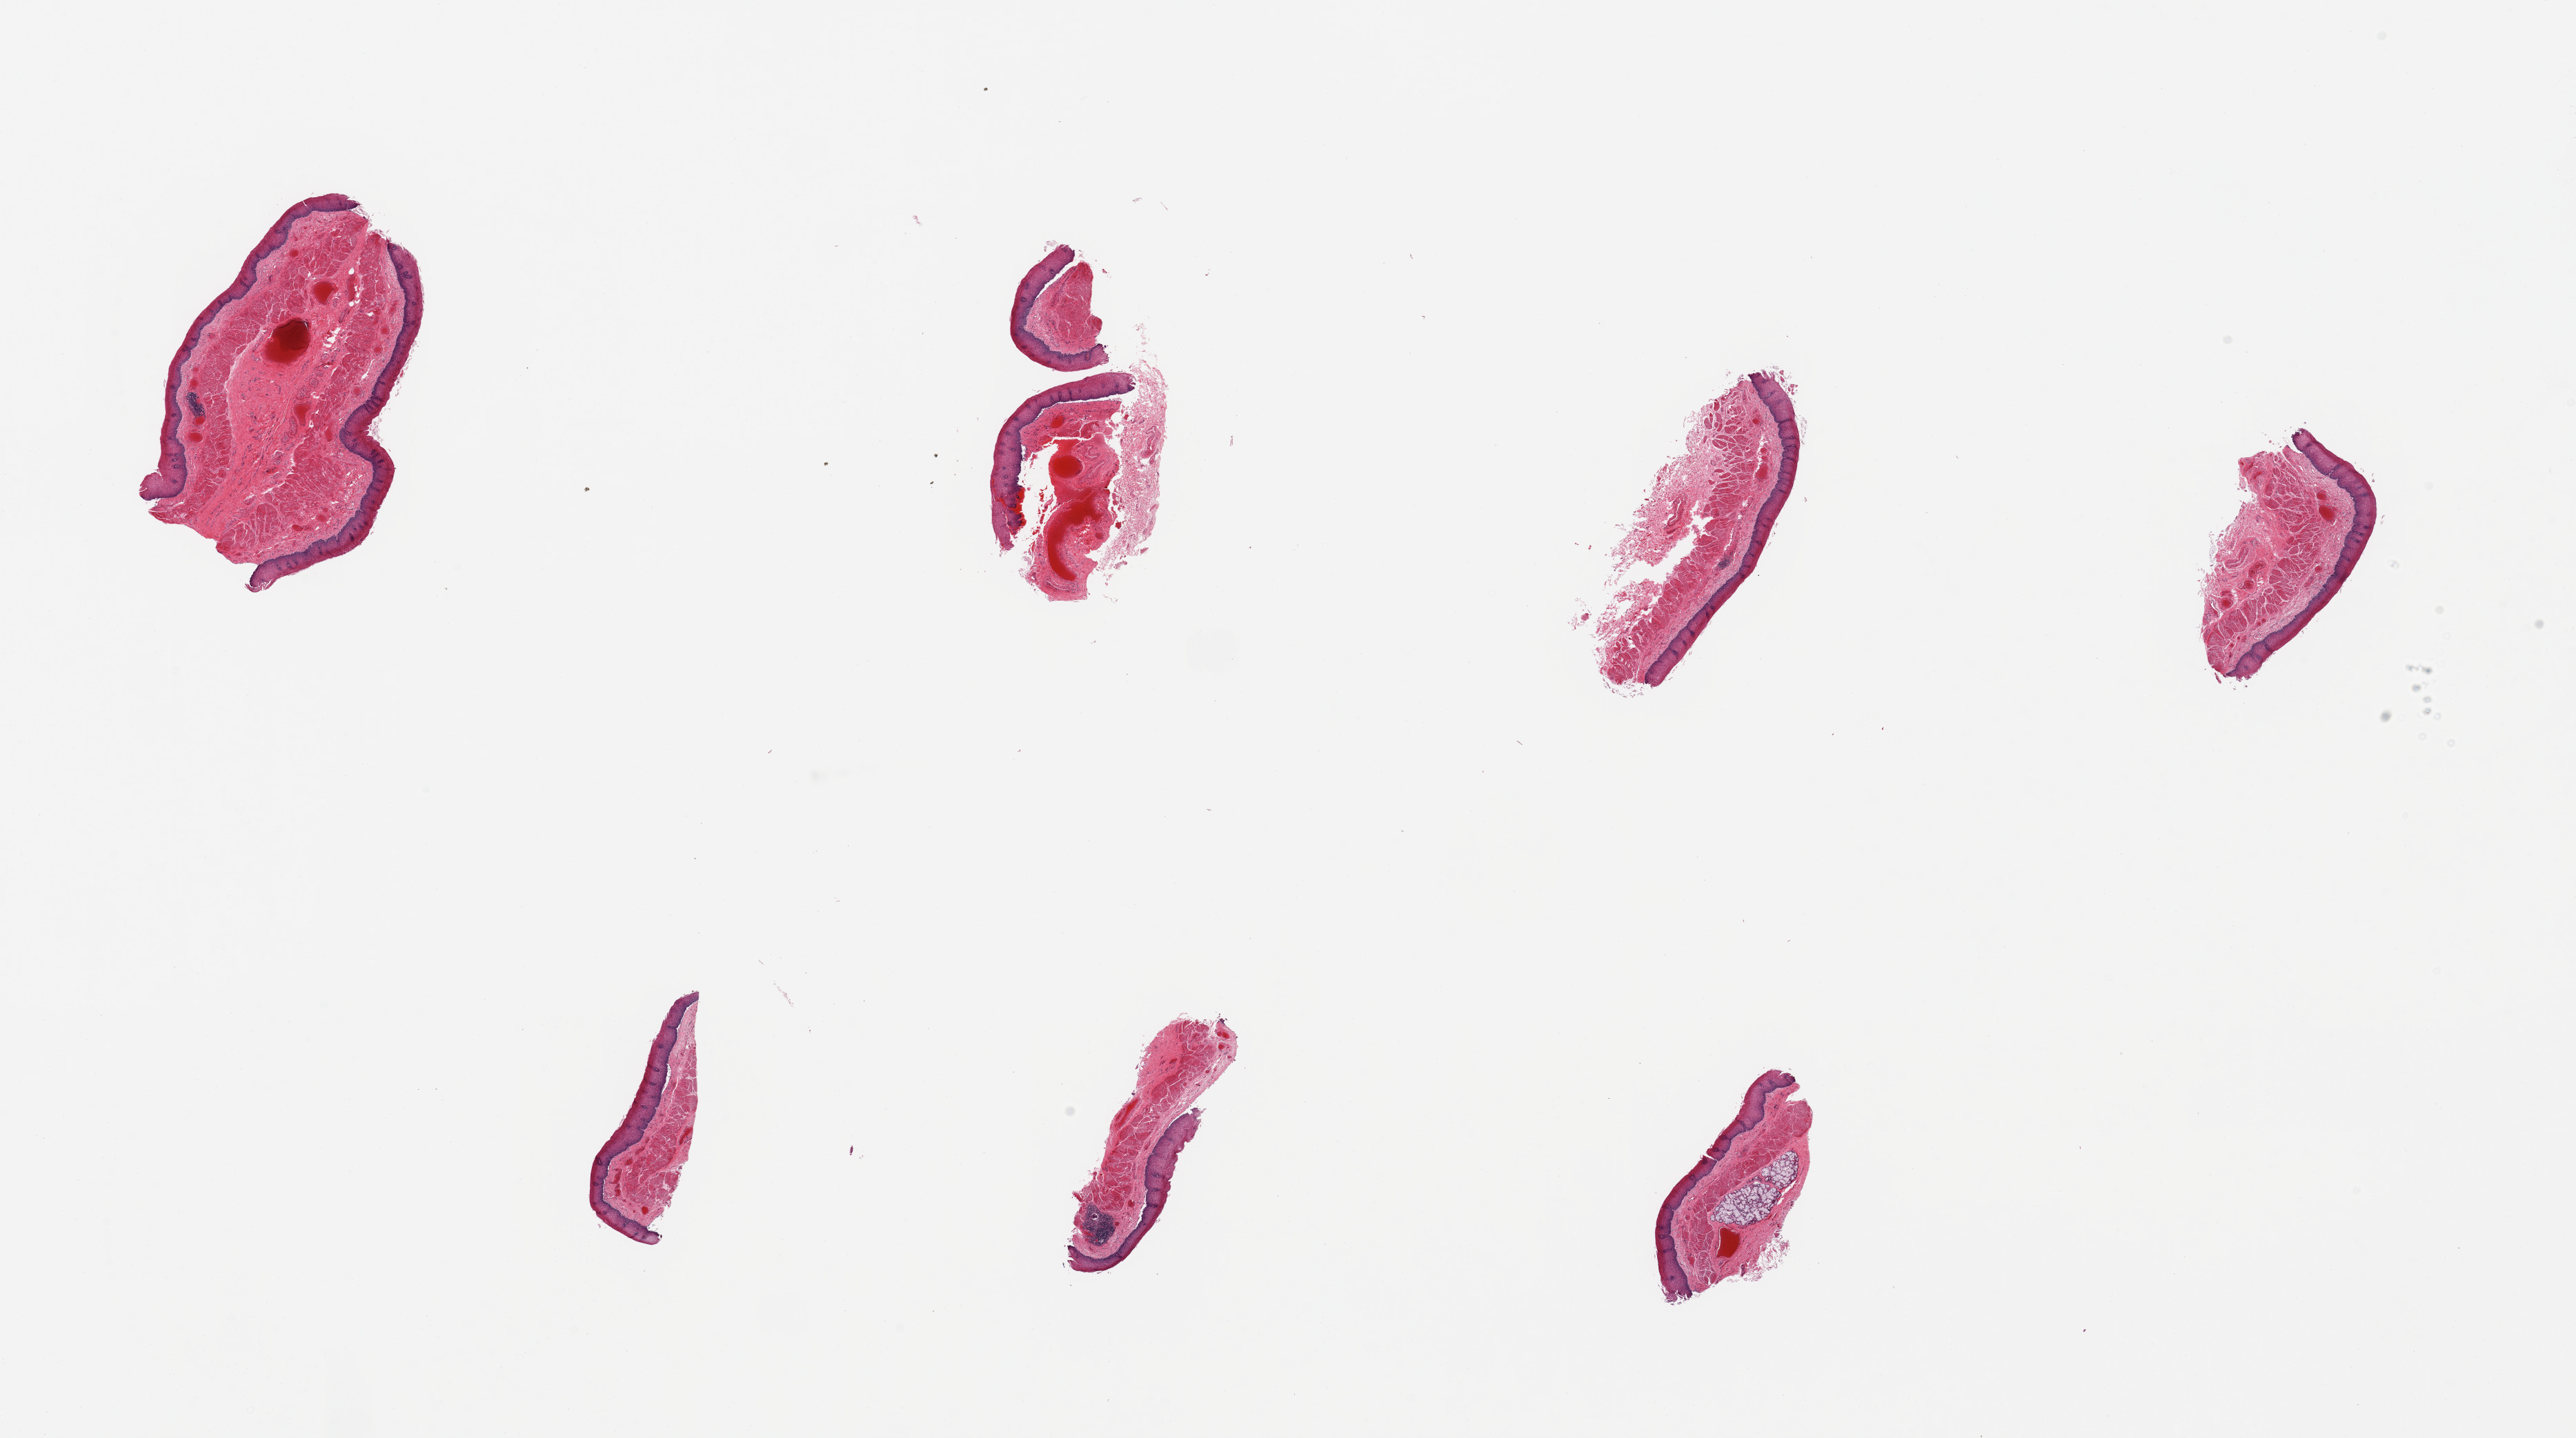
Hematoxylin and eosin (H&E) whole-slide image, shown as a low-resolution overview of the whole scanned area (about 29.5 x 16.5 mm, slide scanned at 20x). PAXgene-fixed, paraffin-embedded tissue. Section of esophageal mucous membrane (target tissue). Donor tissue sample. Male donor.
Pathologist's review note for this sample: 7 pieces; moderate vascular congestion.